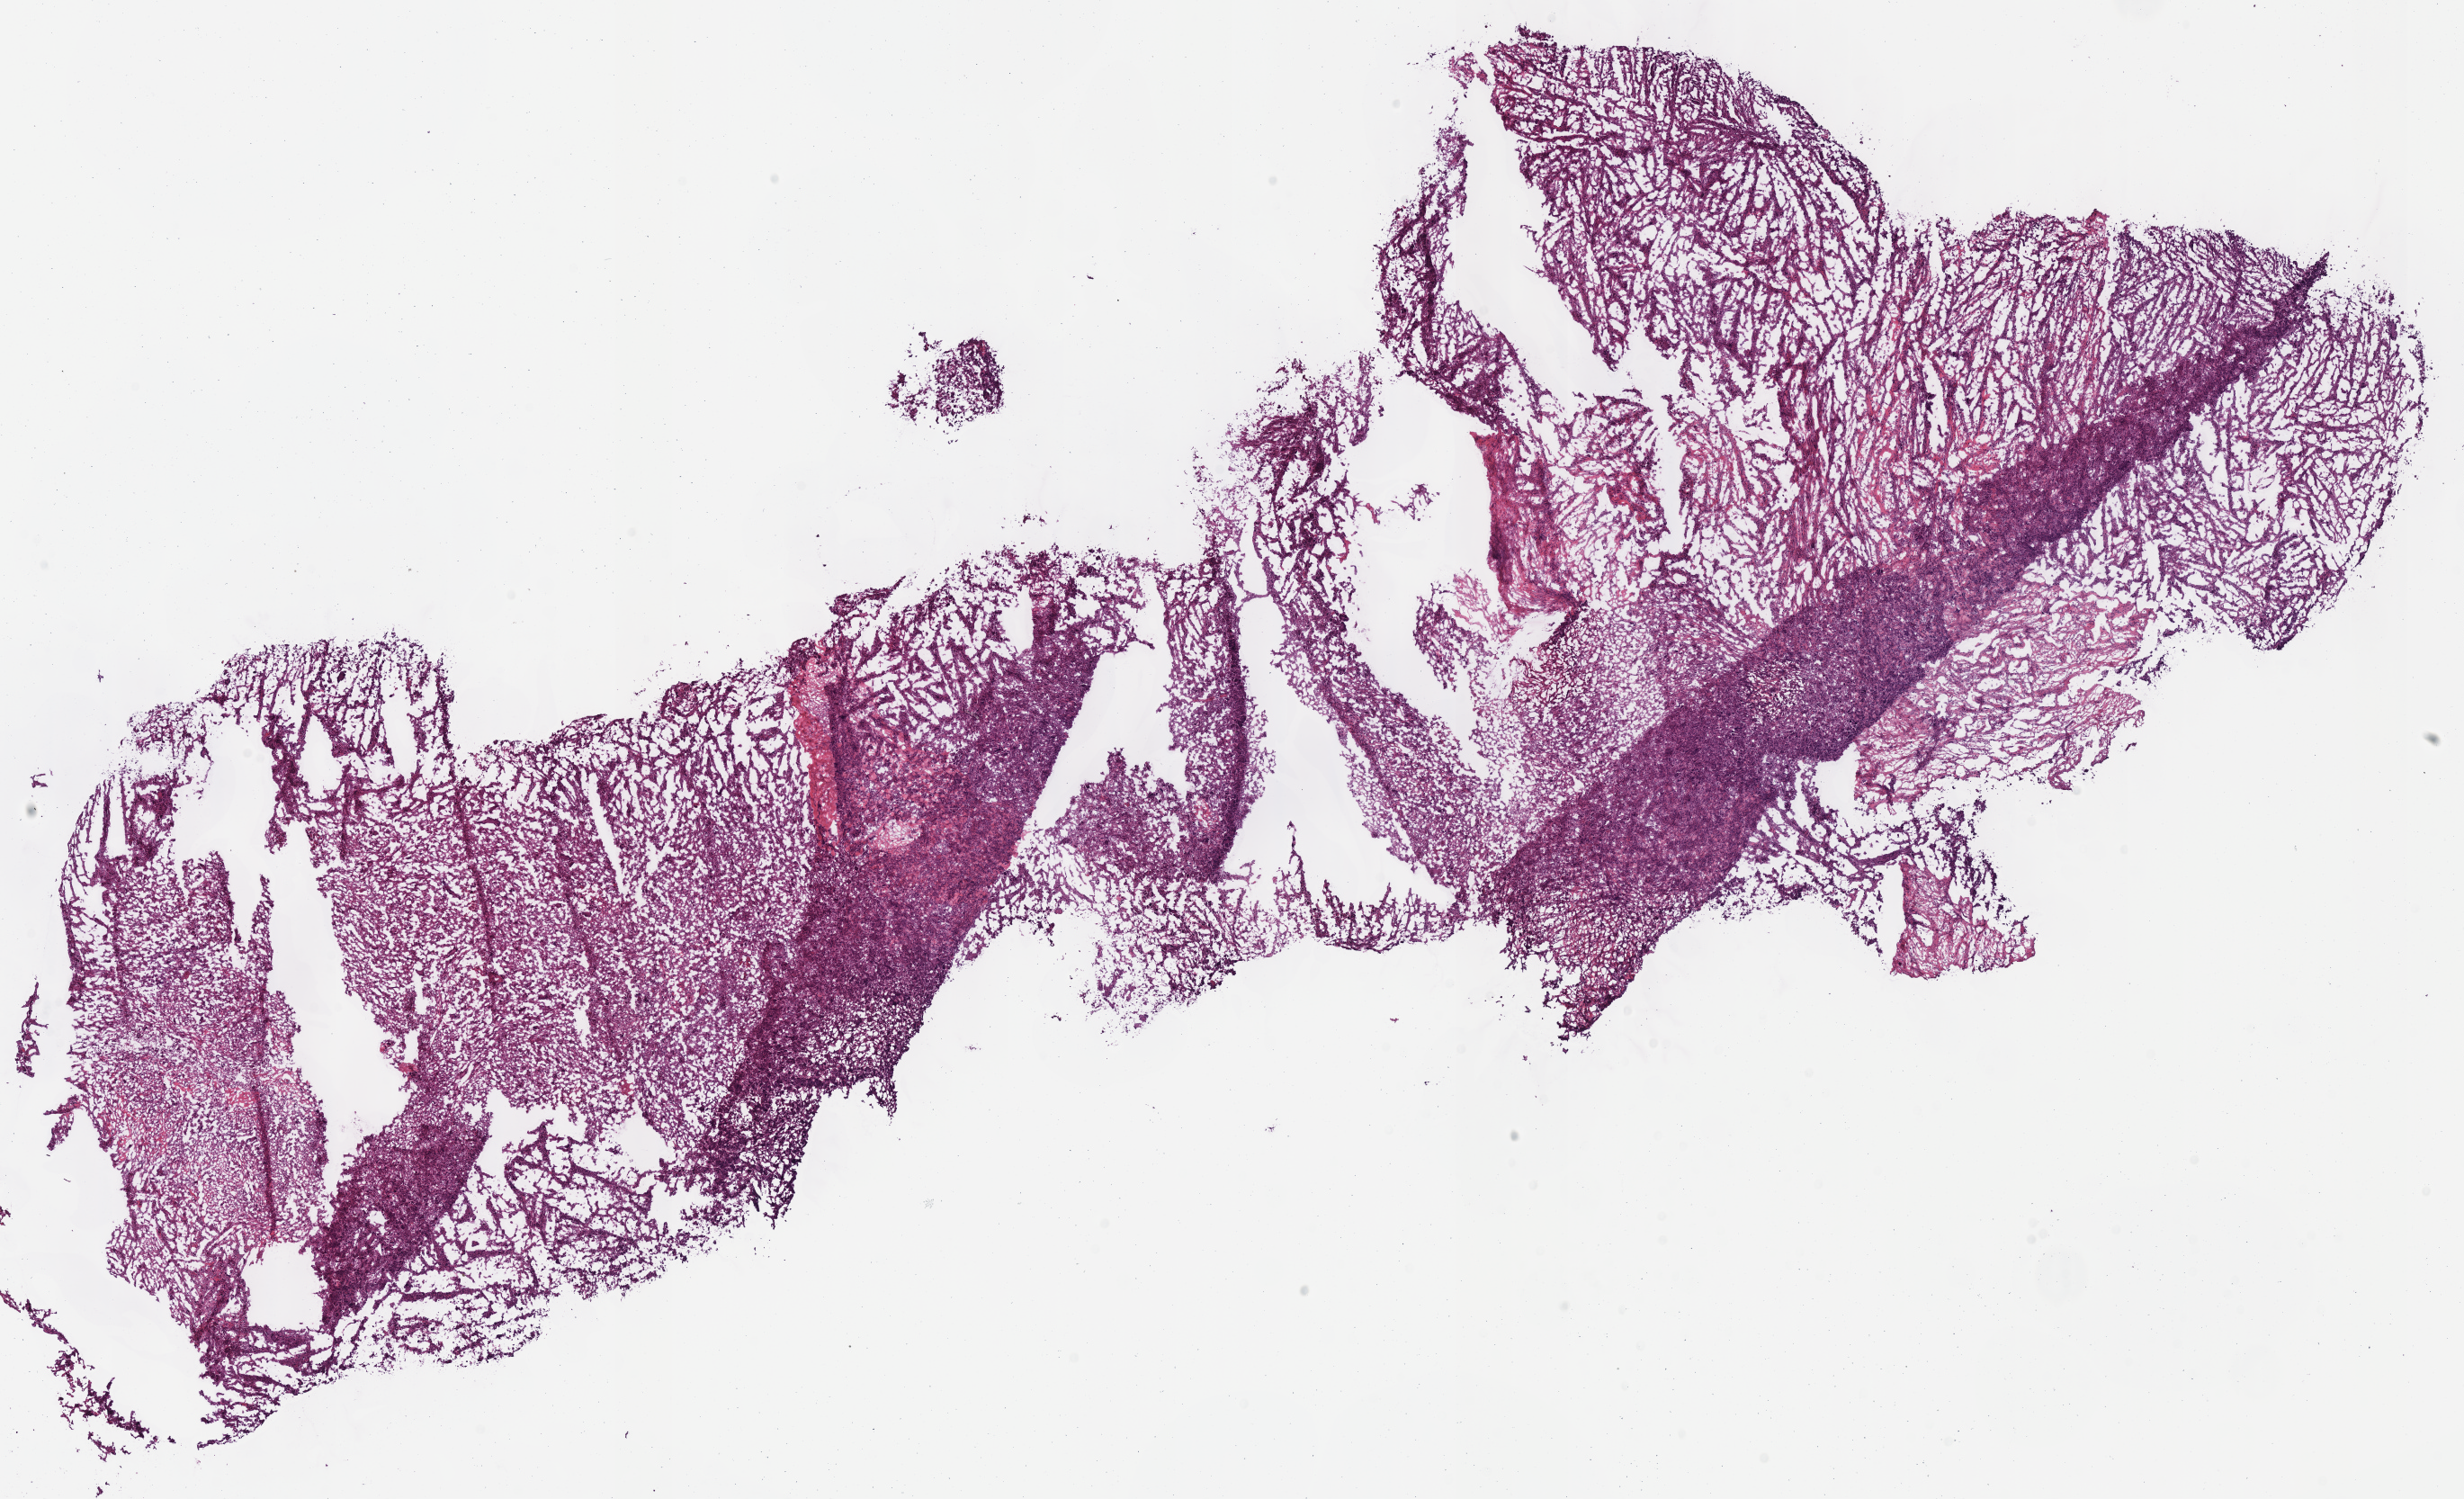
Digitized Hematoxylin and eosin (H&E) stained tissue section (whole slide) — whole scanned area (about 21.5 x 13.1 mm, from a 40x scan) shown as a low-resolution overview; frozen section from the bottom of the tissue portion; kidney, primary tumour sample. Male, age 78 years at initial diagnosis.
Histologic diagnosis: Renal cell carcinoma, chromophobe type.